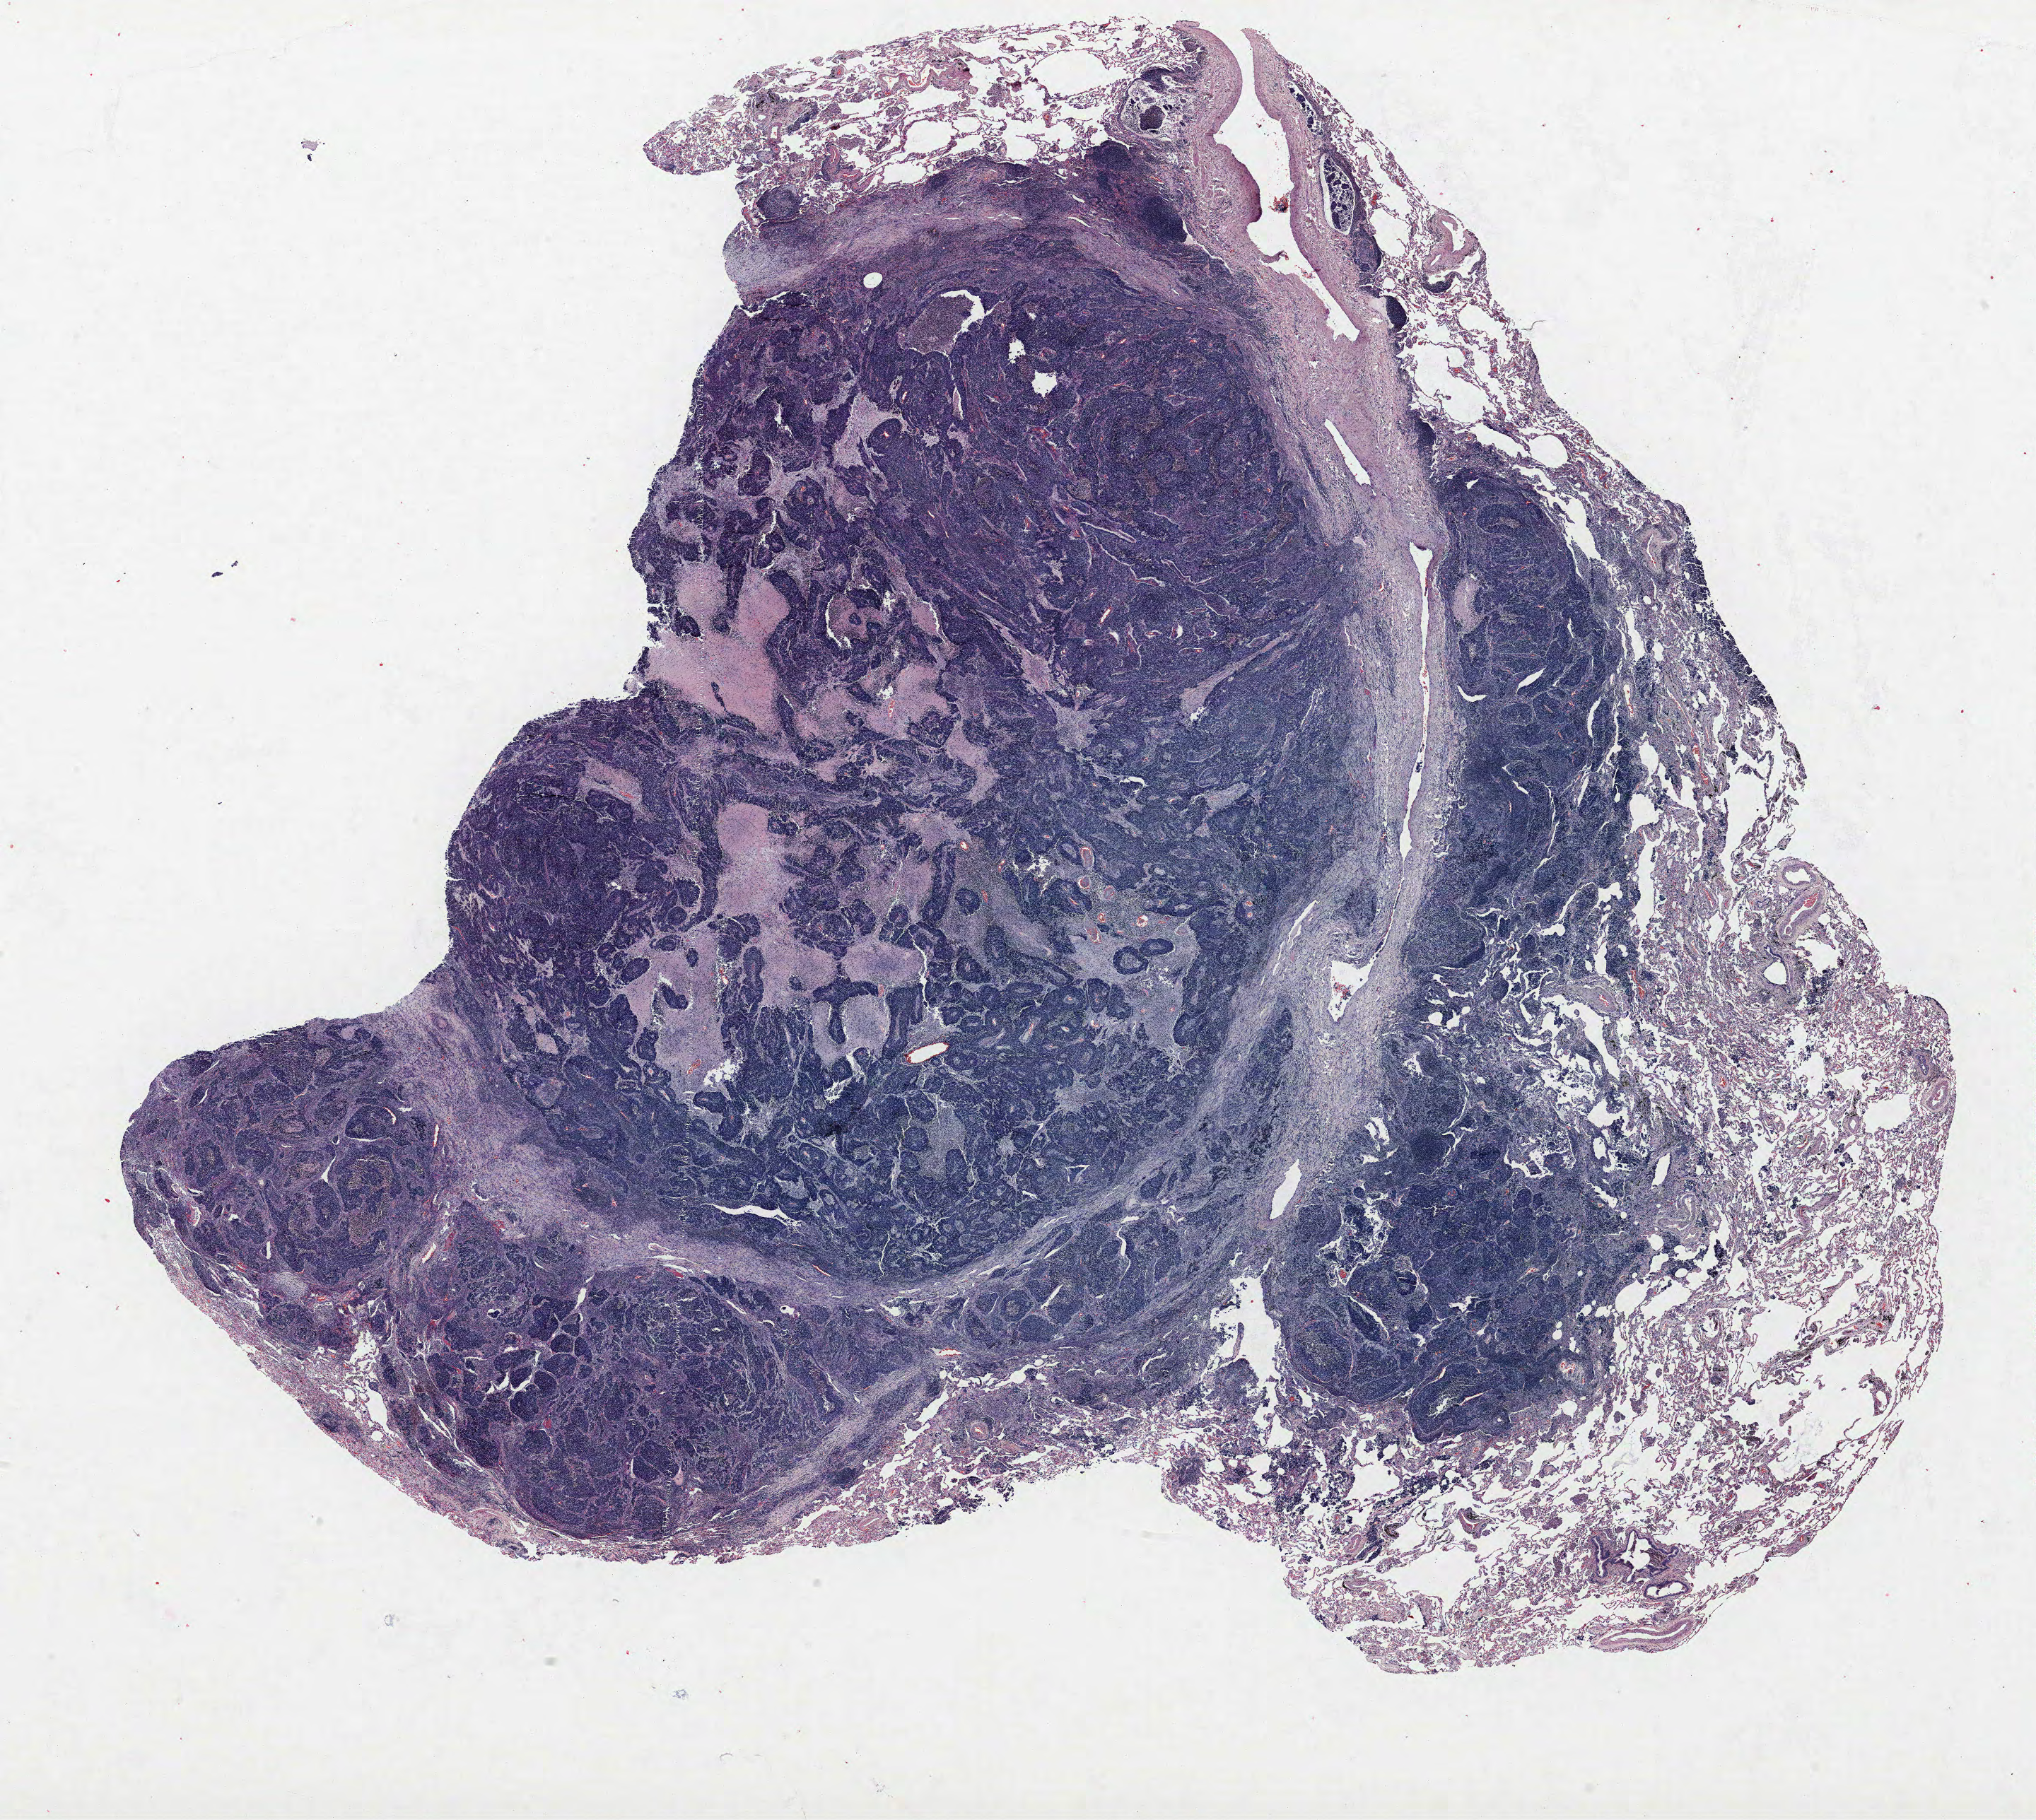
H&E whole-slide image — whole scanned area (about 23.0 x 20.6 mm, from a 40x scan) shown as a low-resolution overview, FFPE section, lung tissue. Male patient, aged 73 at enrolment. Current smoker at enrolment. Grade: poorly differentiated (G3).
* primary tumour location (clinical record): left upper lobe
* participant's lung-cancer diagnosis: Neuroendocrine carcinoma, NOS (ICD-O-3 8246/3)
* stage (AJCC 6th edition): IA
* tumour size (pathology): 26 mm